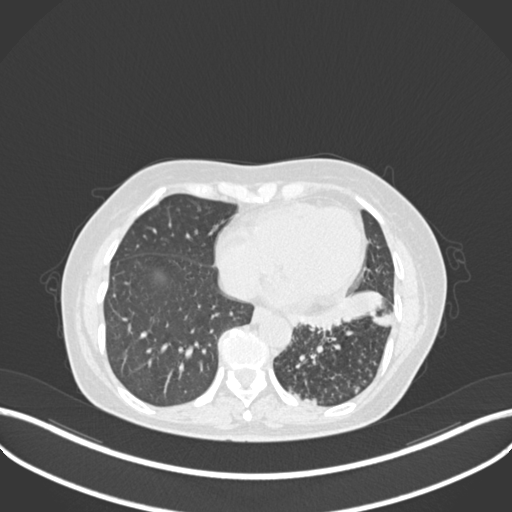
Chest CT, one axial slice; position 89 of 270 along the scan axis; reconstruction kernel B30f; 120 kVp; lung window (W 1500 / L -600 HU); 512 × 512 image matrix, field of view 400 × 400 mm. Female patient, age 63 years. Case-level facts recorded for this patient, not image findings: clinical TNM (as recorded): T1b N0 M0; histopathological grade: G2-3.
Structures marked on this image (rectangle marked by the reading radiologist):
- lung tumour (recorded histology: adenocarcinoma): bounding box <297,285,394,330> (left, top, right, bottom; pixels)